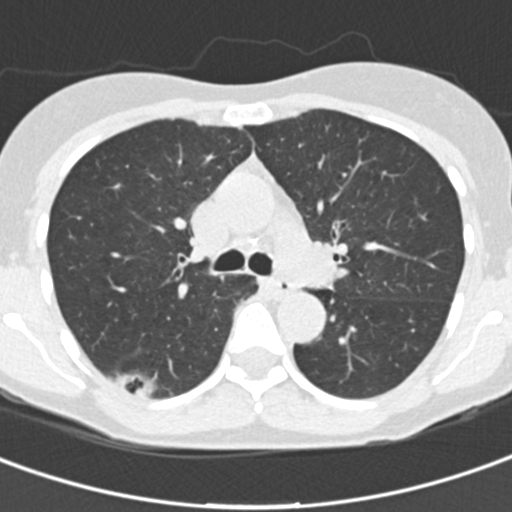
Chest CT (low-dose screening protocol), one axial image. Baseline annual screen. Lung window (W 1500 / L -600 HU). Slice 62 of 162 in the series. 512 × 512 image matrix, field of view 276 × 276 mm. Female participant, aged 64 years at enrolment. Current smoker at enrolment.
Expert-annotated lung lesion, bounding box [x1, y1, x2, y2] px = [86, 349, 178, 418]. Reader record for this screening exam (exam-level; its link to the box is not recorded): non-calcified nodule or mass ≥4 mm, right lower lobe, 31 × 15 mm, poorly defined margins, ground glass attenuation. Official screen result: positive, change unspecified: nodule(s) >= 4 mm or enlarging nodule(s), mass(es), or other non-specific abnormalities suspicious for lung cancer. Lung cancer was diagnosed 91 days after this screen: bronchiolo-alveolar carcinoma, non-mucinous, right lower lobe, well differentiated (G1), stage IA (AJCC 6th edition), 20 mm at pathology.